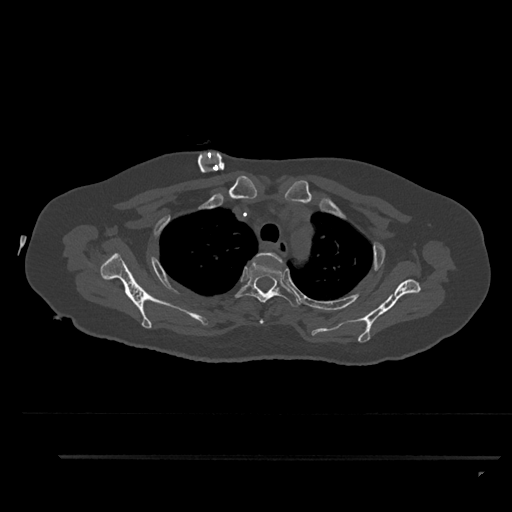
CT including the spine, one axial slice. Position 692 of 797 along the scan axis. Bone window (W 1800 / L 400 HU). 0.5 mm slice thickness. 512 × 512 image matrix, field of view 408 × 408 mm. Patient: female, 44 years. Case-level facts recorded for this patient, not image findings: primary cancer: renal; vertebrae with lytic lesions (as recorded): L1.
Annotated regions visible in this slice (semi-automatically segmented with operator editing):
- T2 vertebra: bounding box <256,252,283,324> (left, top, right, bottom; pixels)
- T3 vertebra: <235,260,302,307>